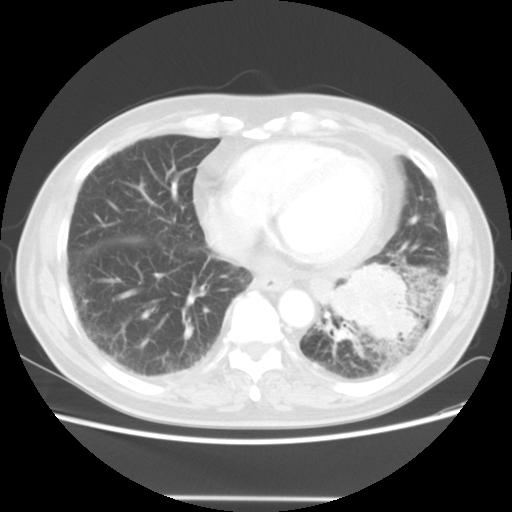
Chest CT, one axial slice; slice 16 of 56 in the series (ordered by position); reconstruction kernel STANDARD; lung window (W 1500 / L -600 HU); 5 mm slice thickness; 512 × 512 image matrix, field of view 360 × 360 mm. Male patient, age 66 years. From the clinical record (not read from this slice): clinical TNM (as recorded): T4 N3 M0; histopathological grade: G3.
Annotated regions visible in this slice (rectangle marked by the reading radiologist):
- lung tumour (recorded histology: small cell carcinoma): bounding box <325,253,425,362> (left, top, right, bottom; pixels)